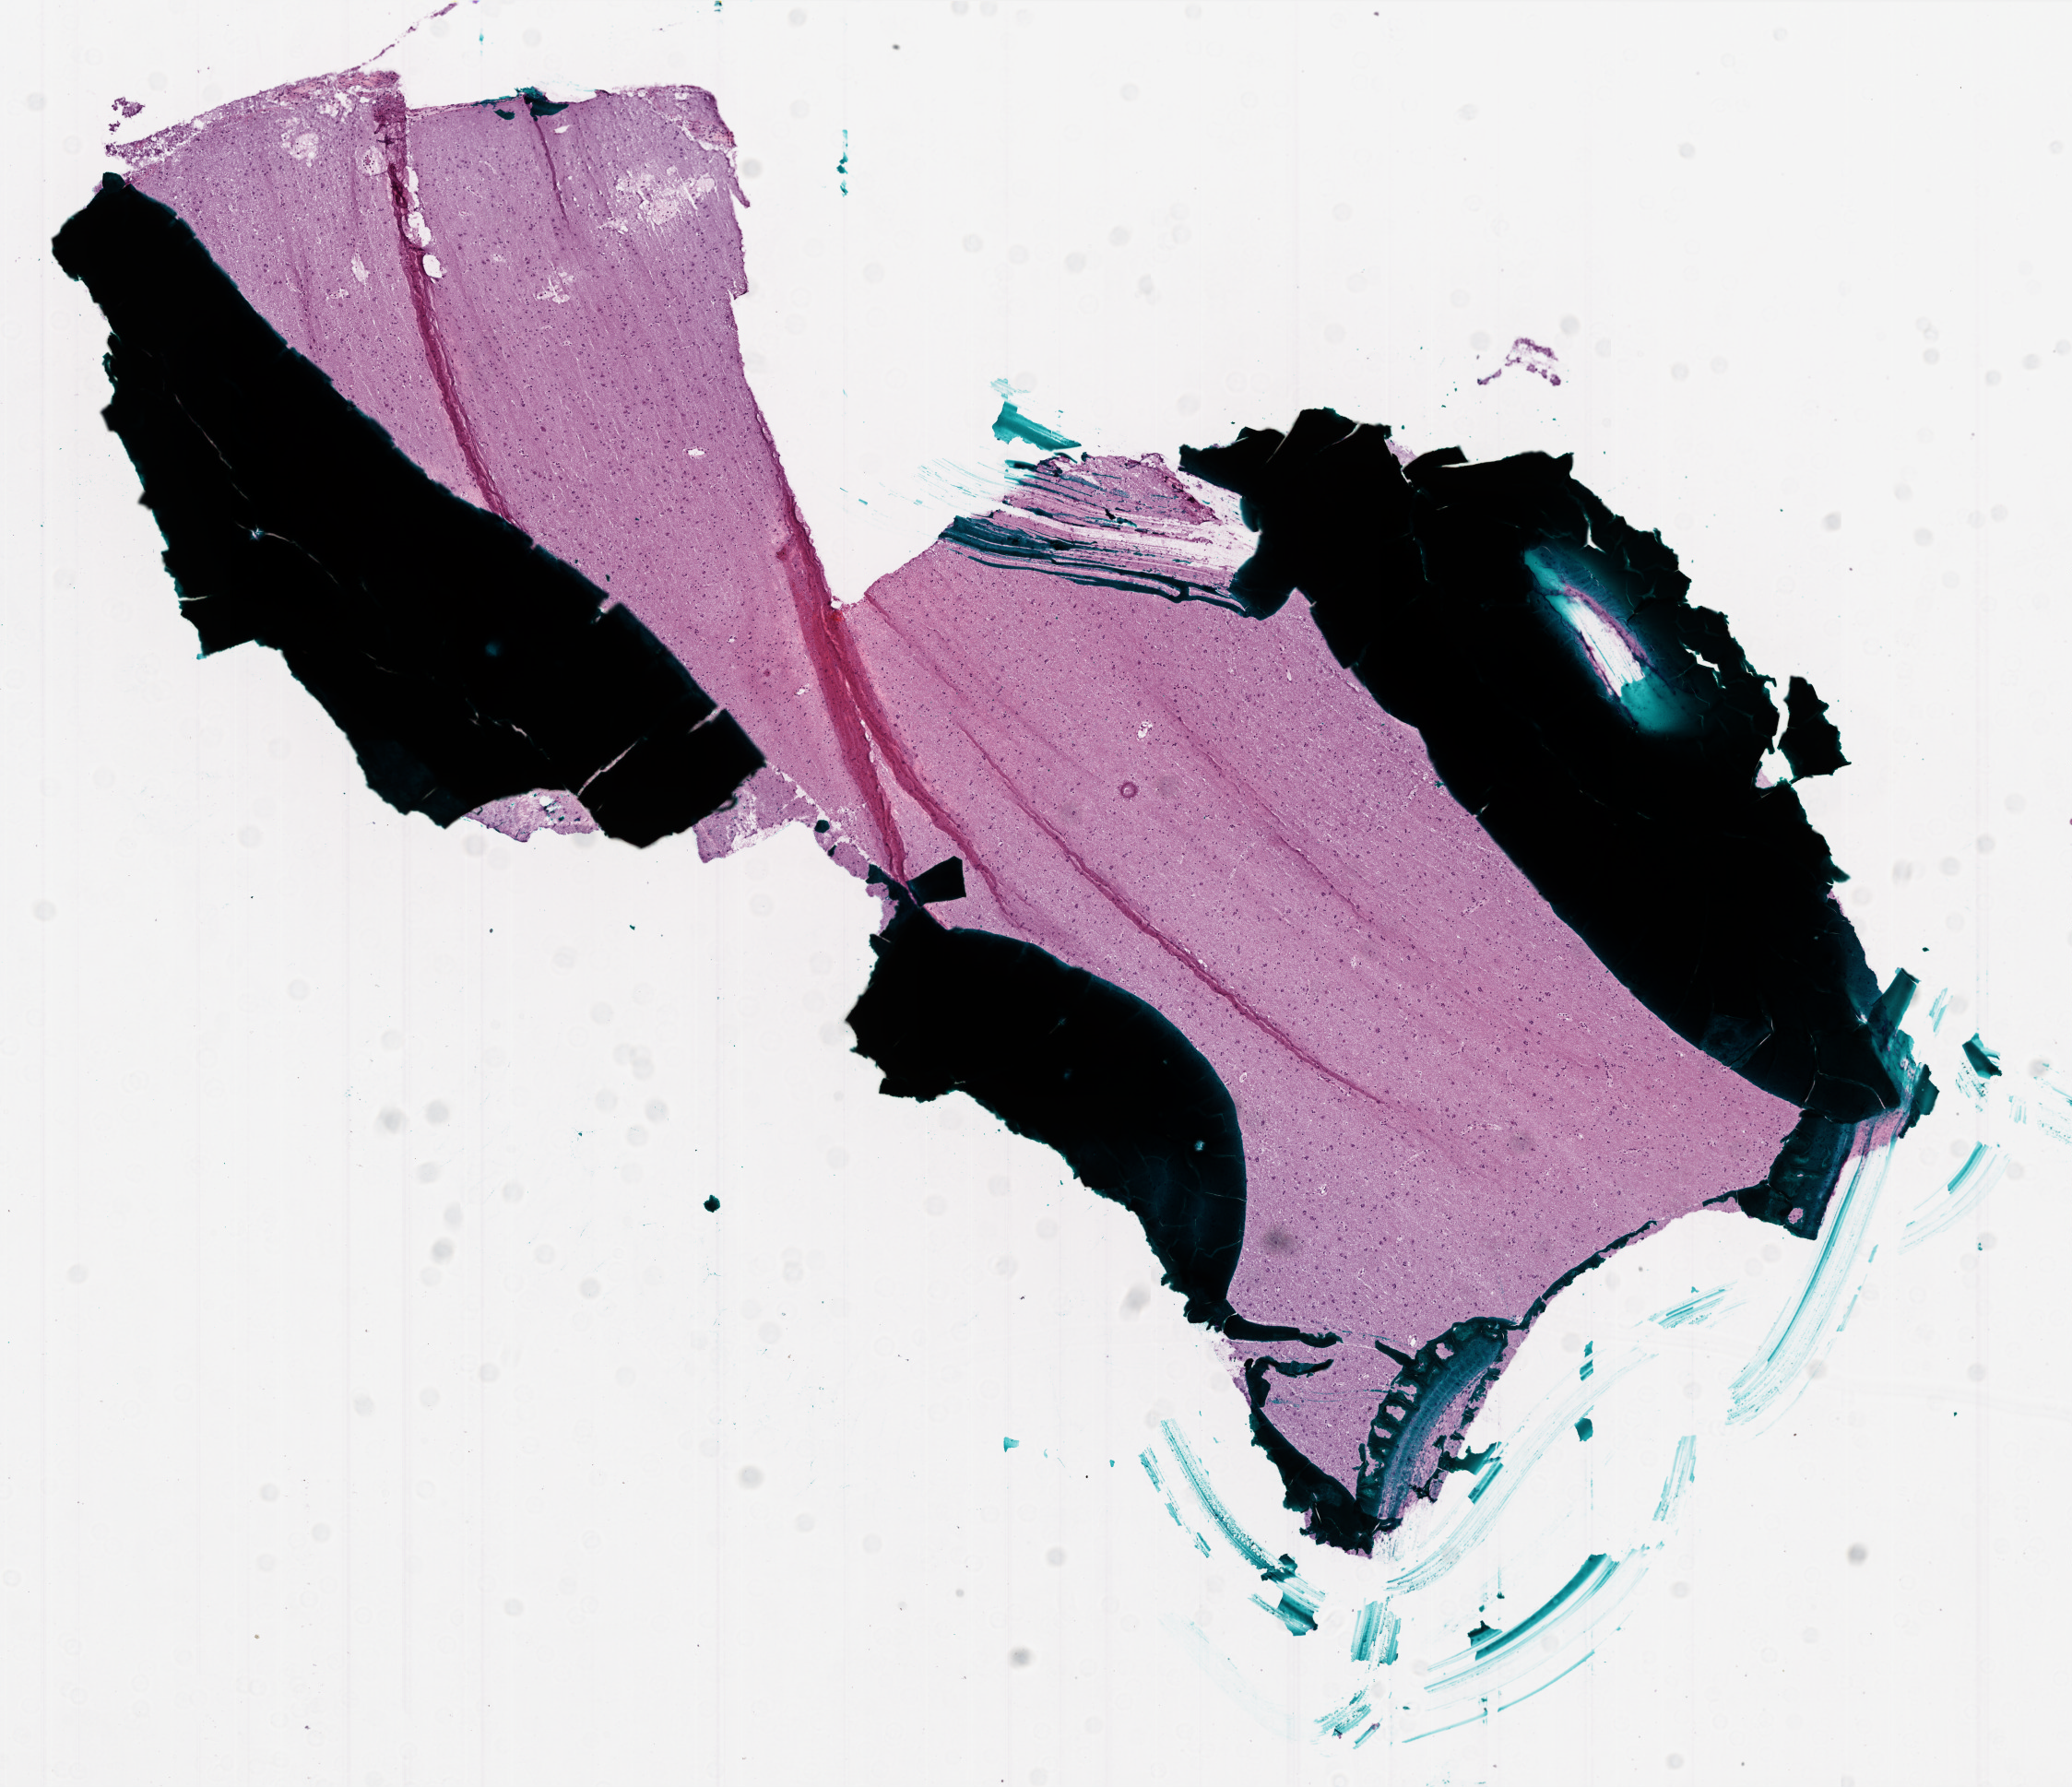
Whole-slide histology image, H&E, low-resolution overview of the scanned area, about 9.0 x 7.8 mm, frozen section from the bottom of the tissue portion, sample: primary tumour, brain. Male, age 44 years at initial diagnosis. Composition of this section per pathologist review: tumour cells 0%, tumour nuclei 0%, normal cells 100%, stromal cells 0%, necrosis 0%.
Diagnosis: Glioblastoma.